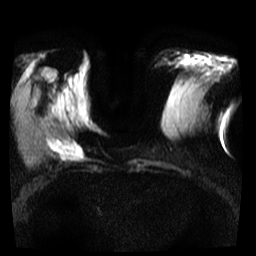
Breast MRI, one axial slice; position 11 of 35 along the scan axis; diffusion-weighted series; image 2 of 4 stored at this slice position (different b-values; order by instance number); 3 T; 5 mm slice thickness; 256 × 256 image matrix, field of view 300 × 300 mm. Female patient.
Annotated regions visible in this slice (outlined manually by an expert reader):
- tumour on diffusion-weighted imaging: box from (x=47, y=138) to (x=83, y=159) px